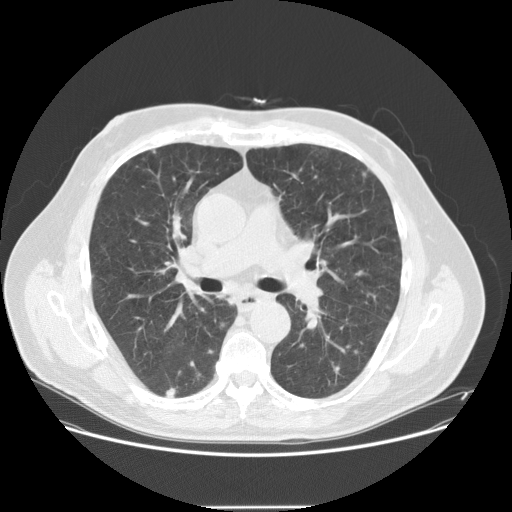
Low-dose screening chest CT, one axial slice. Slice 86 of 143 in the series (ordered by position). Lung window (W 1500 / L -600 HU). 2.5 mm slice thickness. 512 × 512 image matrix, field of view 400 × 400 mm.
Outlined on this slice (manually delineated by an expert):
- lesion 3 (tumor, lower lobe of right lung): bounding box <165,387,175,397> (left, top, right, bottom; pixels)